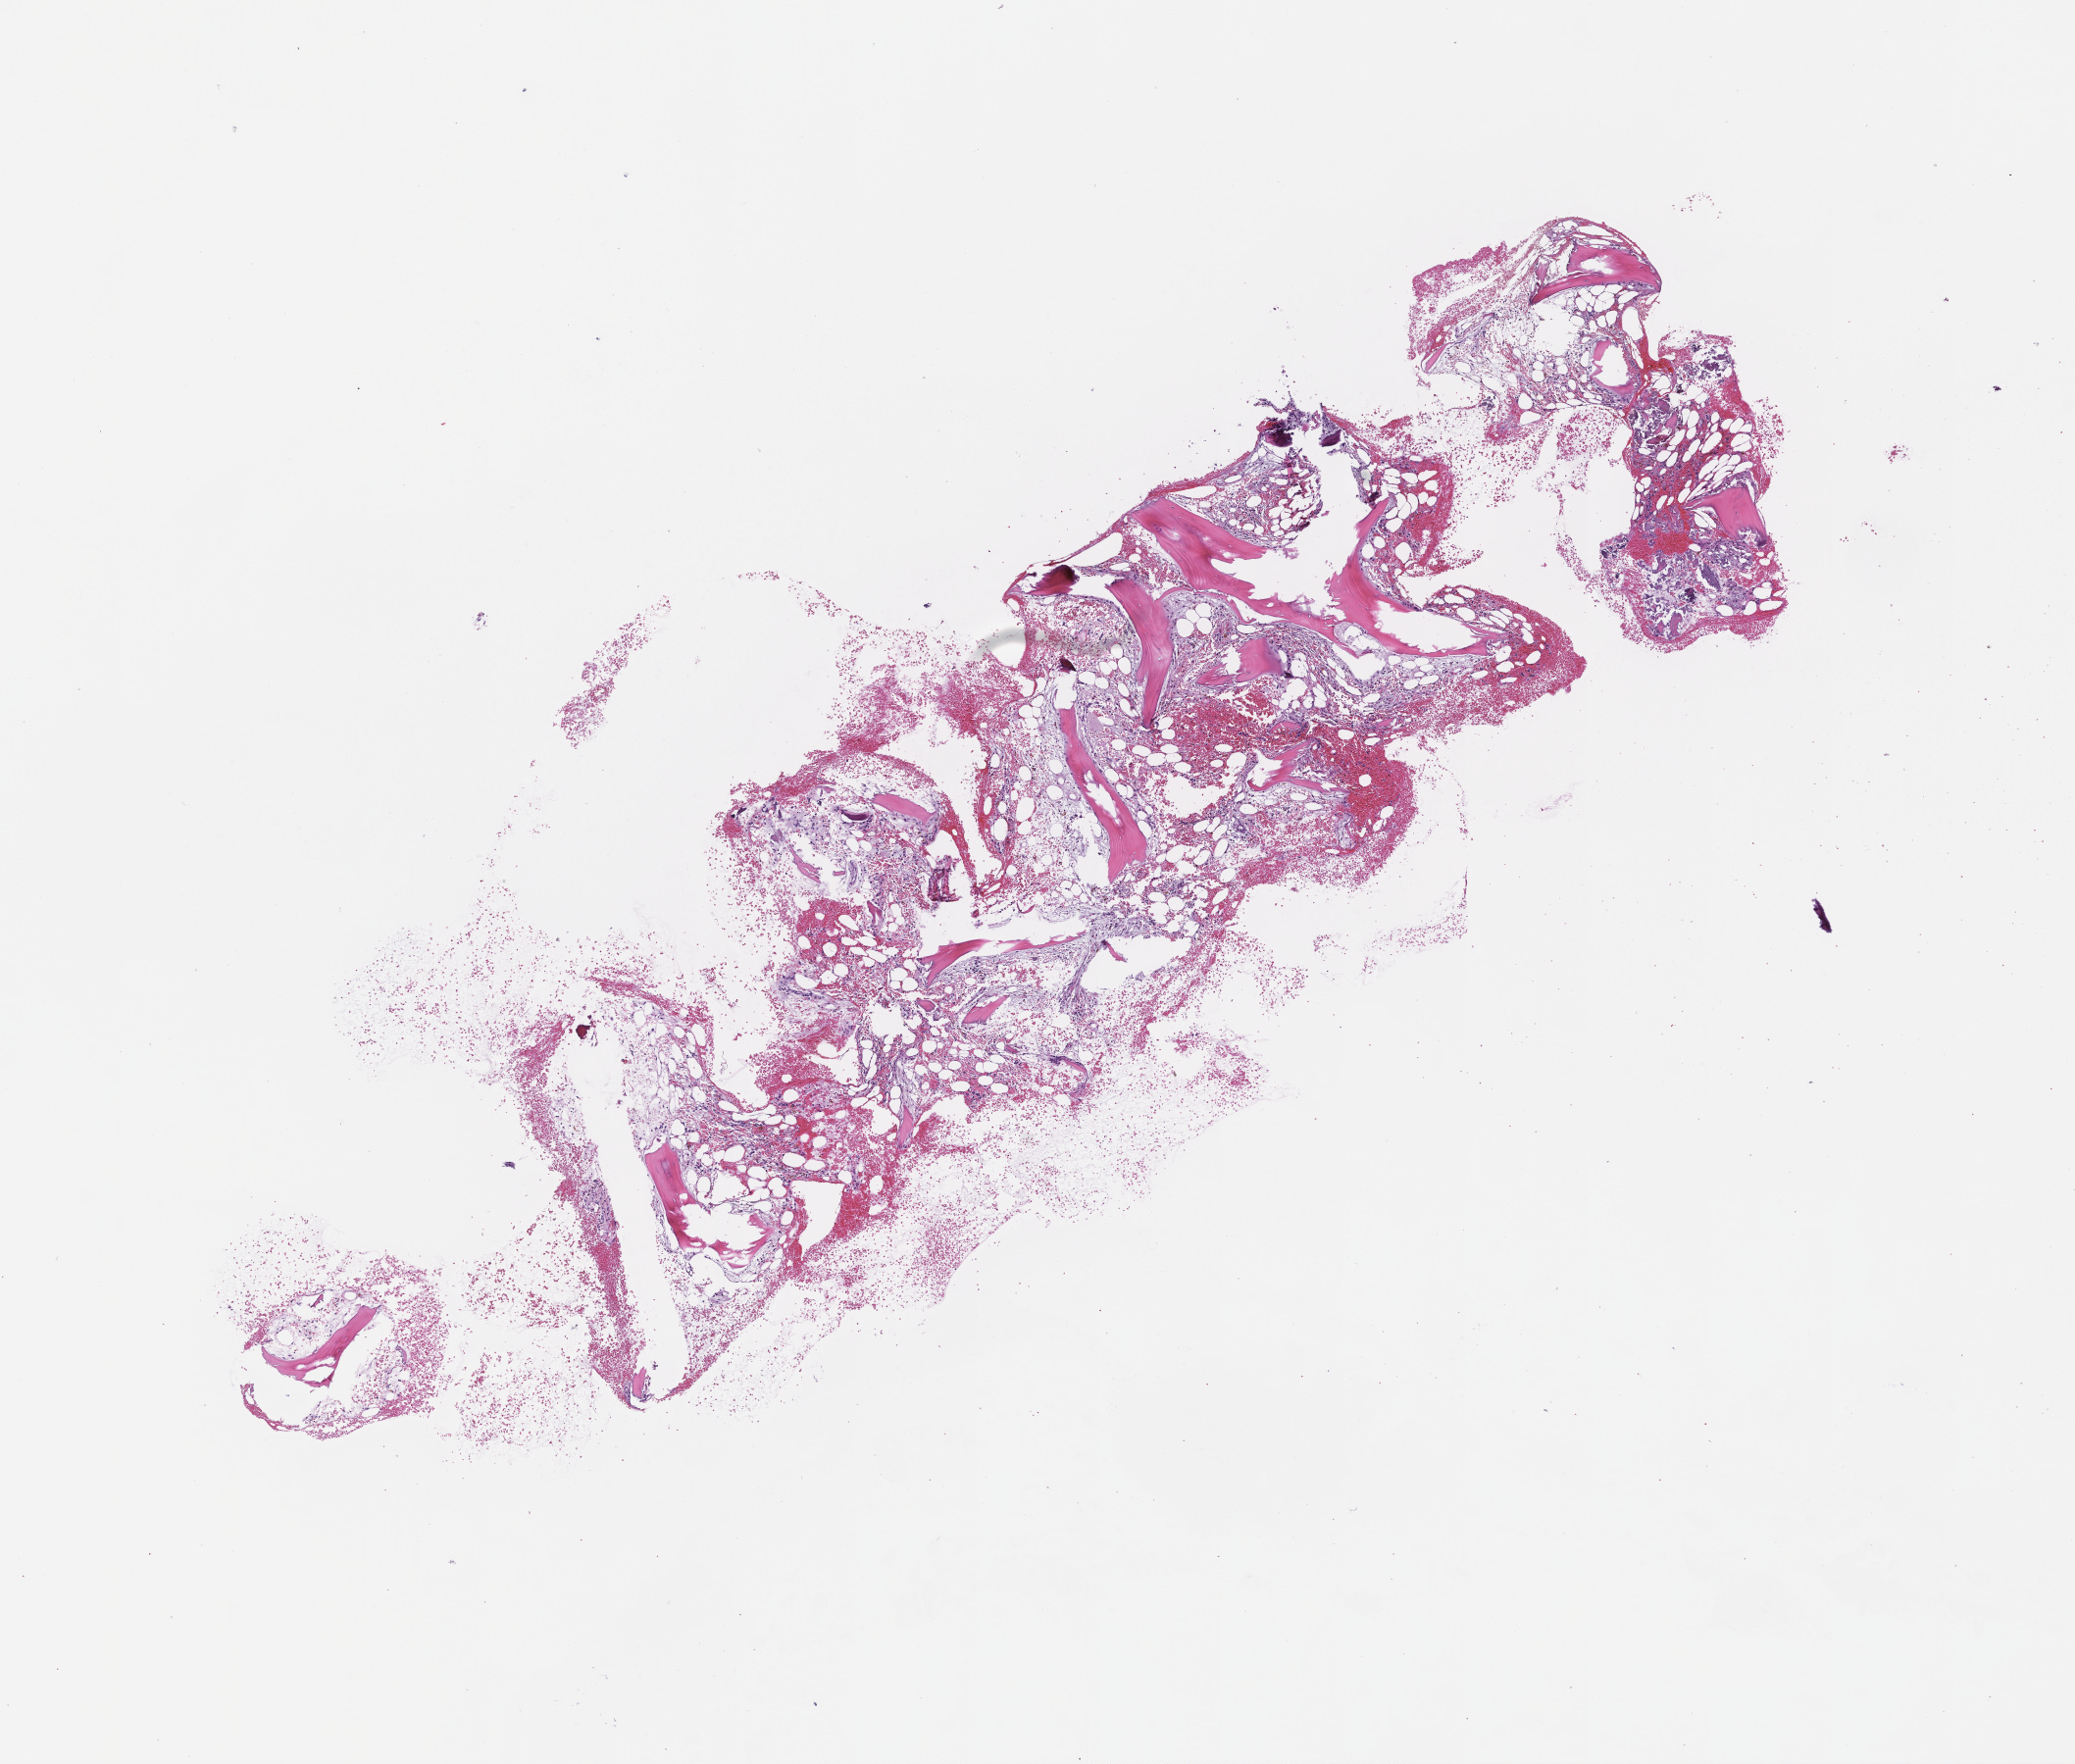
Whole-slide image, H&E stain — low-resolution overview of the scanned area, about 8.5 x 7.3 mm; formalin-fixed paraffin-embedded section; tissue site: bone marrow. Patient sex: female.
This section: primary tumour tissue. Diagnosis: Acute Myeloid Leukemia Not Otherwise Specified.